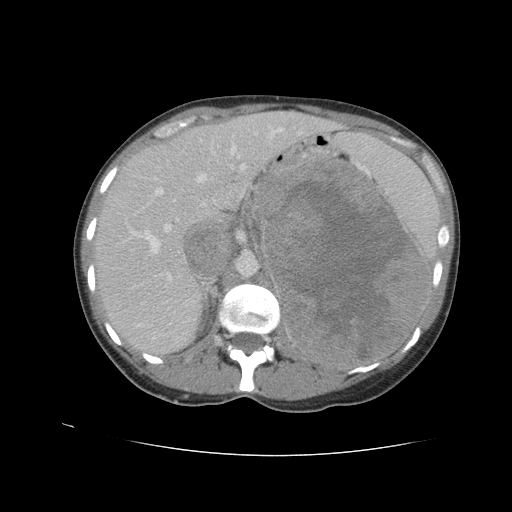
Contrast-enhanced abdominal CT, one axial slice. Slice 68 of 90 in the series (ordered by position). 120 kVp. Intravenous contrast given. Soft-tissue window (W 400 / L 40 HU). 5 mm slice thickness. 512 × 512 image matrix, field of view 360 × 360 mm. Female patient. From the clinical record (not read from this slice): diagnosis: adrenocortical carcinoma; tumour side: left adrenal; tumour size at pathology: 18 cm; Ki-67 index: 11 %; stage (as recorded): 3.
Outlined on this slice (semi-automatically segmented with operator editing):
- mass: box from (x=257, y=158) to (x=430, y=365) px